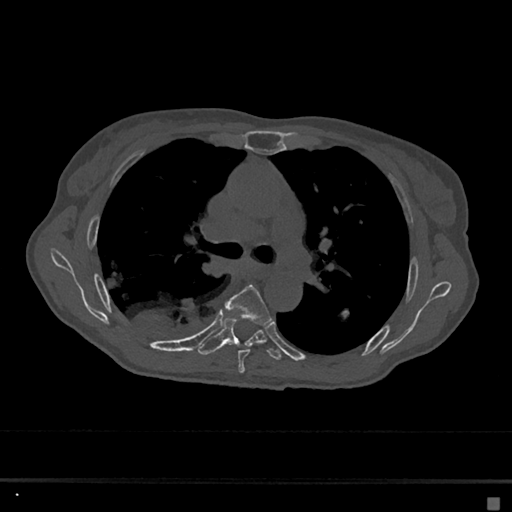
CT including the spine, one axial slice; position 441 of 797 along the scan axis; 120 kVp; bone window (W 1800 / L 400 HU); 0.5 mm slice thickness; 512 × 512 image matrix. Female patient, age 68 years. From the clinical record (not read from this slice): primary cancer: renal.
Outlined on this slice (semi-automatically segmented with operator editing):
- T5 vertebra: bounding box <225,284,272,374> (left, top, right, bottom; pixels)
- T6 vertebra: <197,318,282,360>